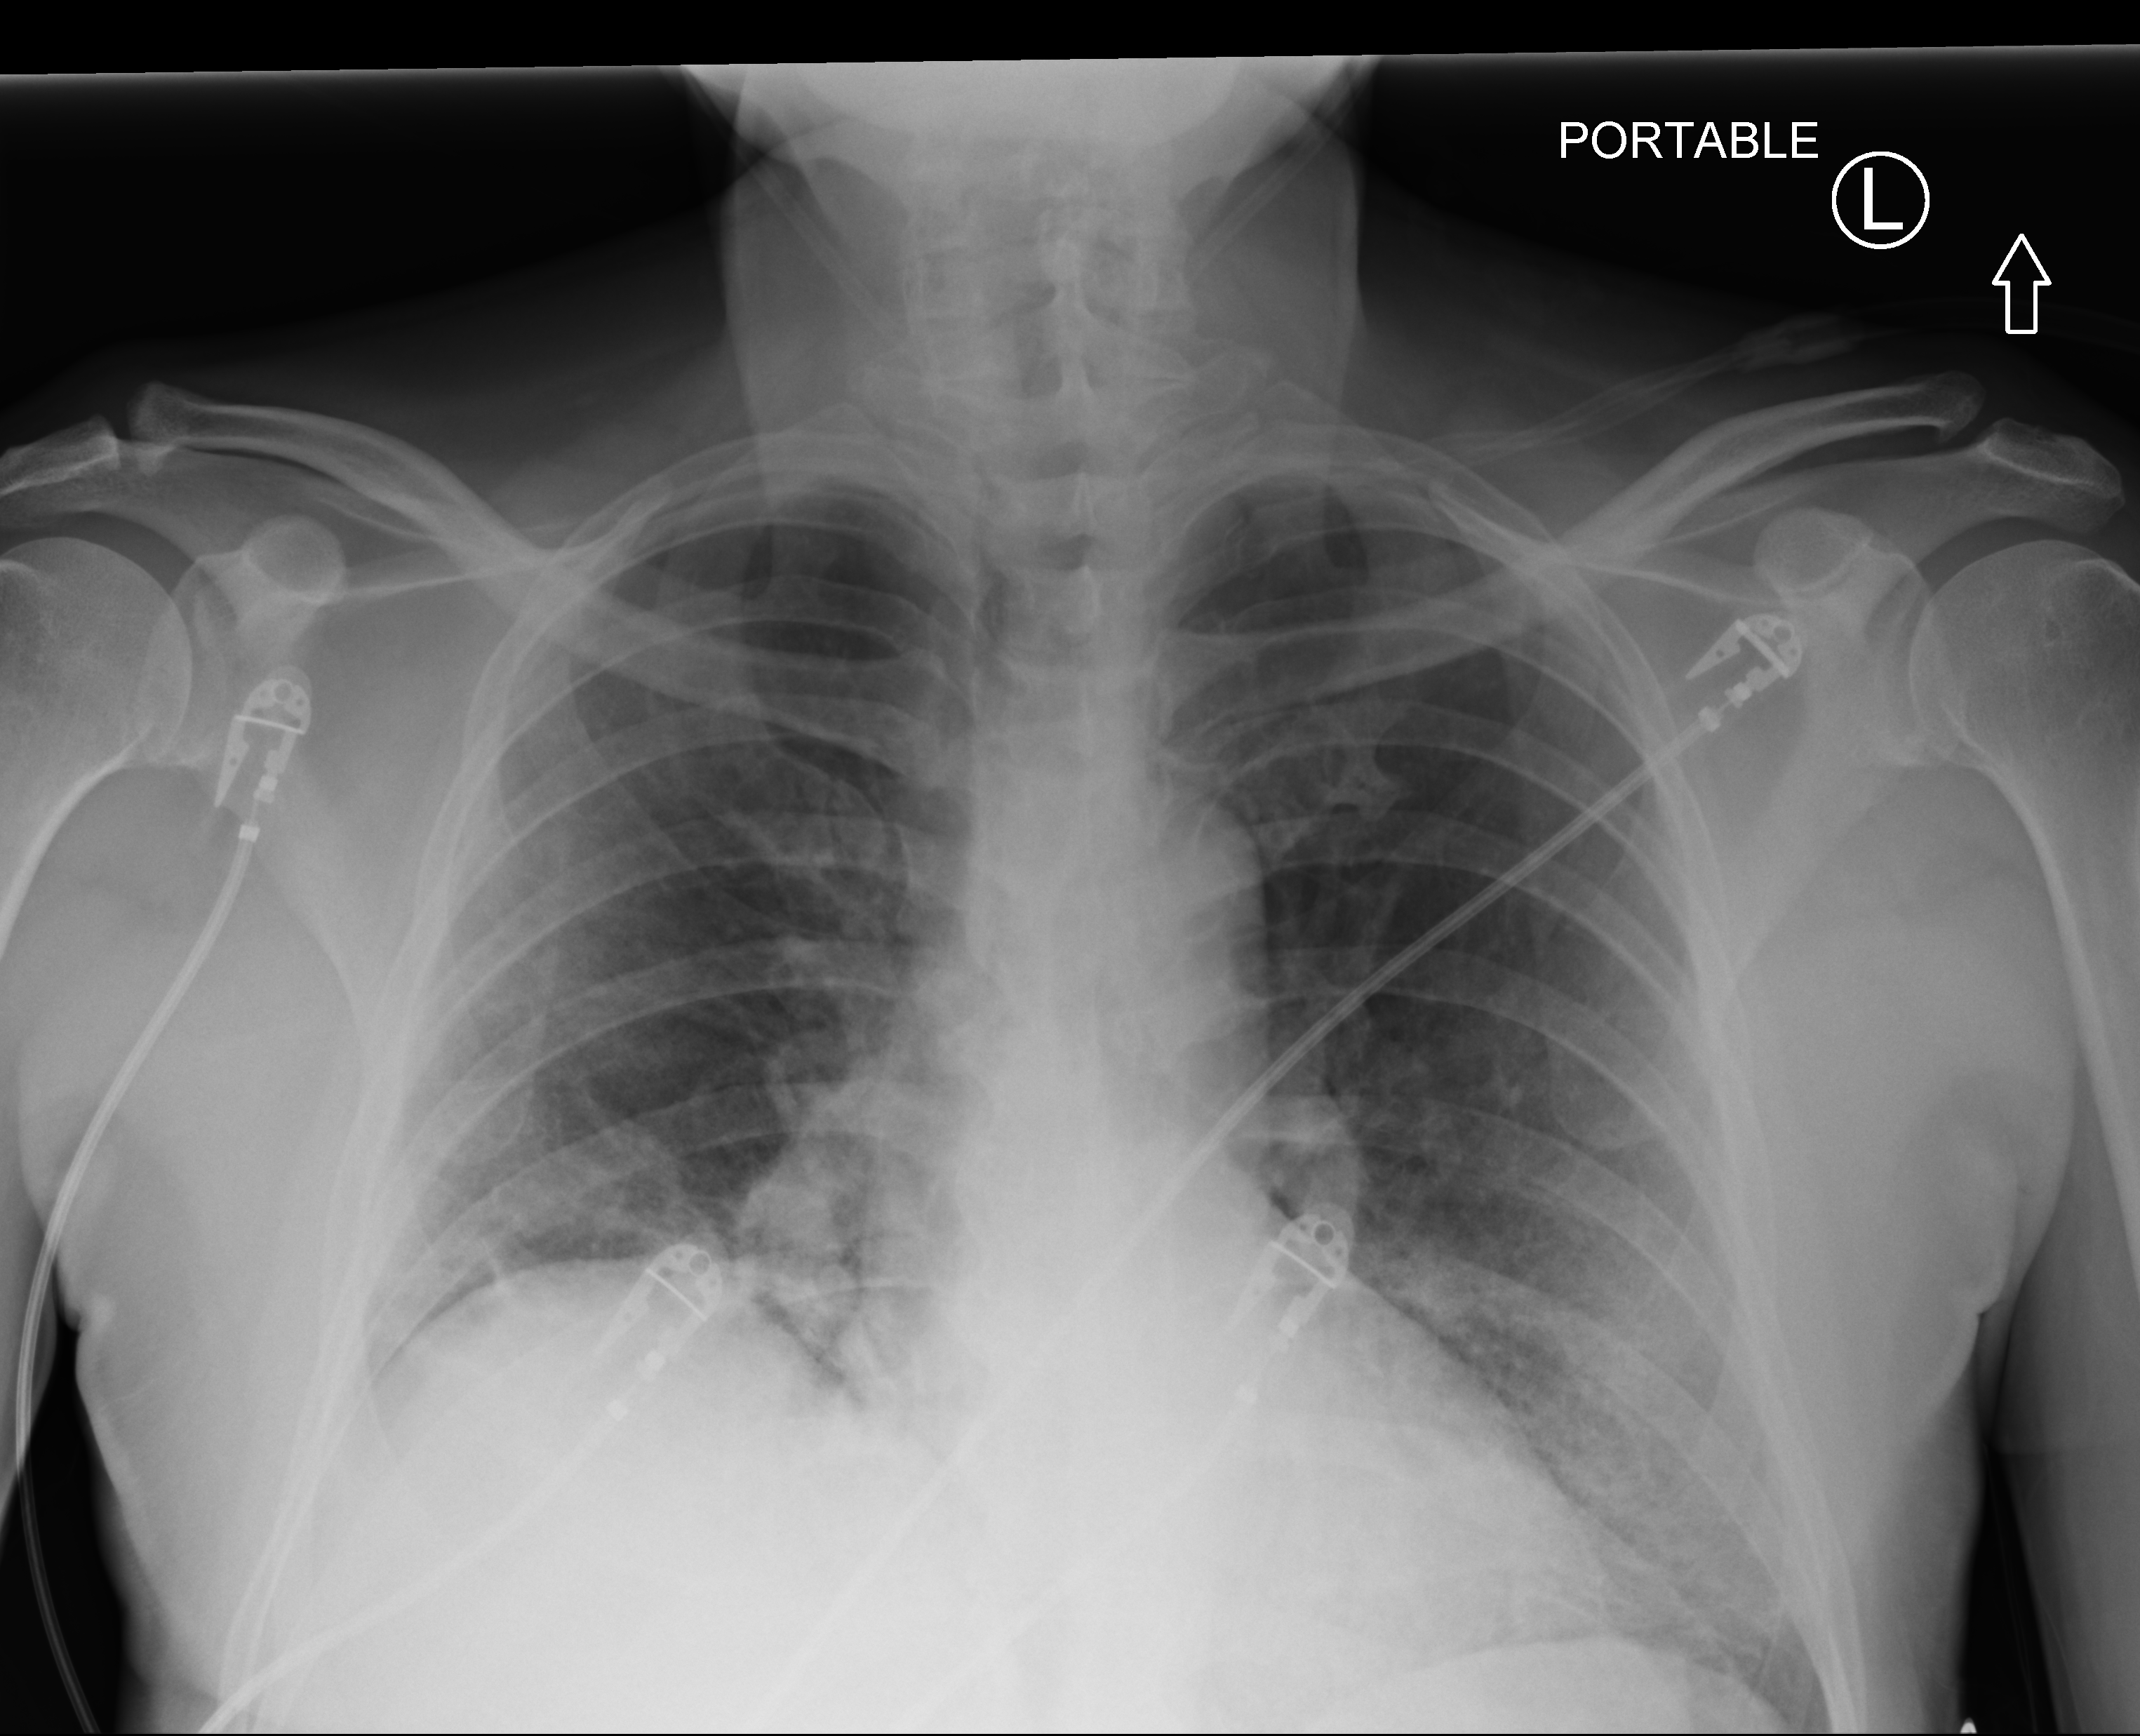
Chest X-ray (portable); anteroposterior (AP) projection. Patient hospitalised with COVID-19; male, aged 60–74 years.
Hospital-stay facts (about this admission, not read from this image; timing relative to this image not recorded): length of hospital stay: 18 days; other chronic lung disease (admission record): no; admitted to intensive care during this hospital stay: yes.